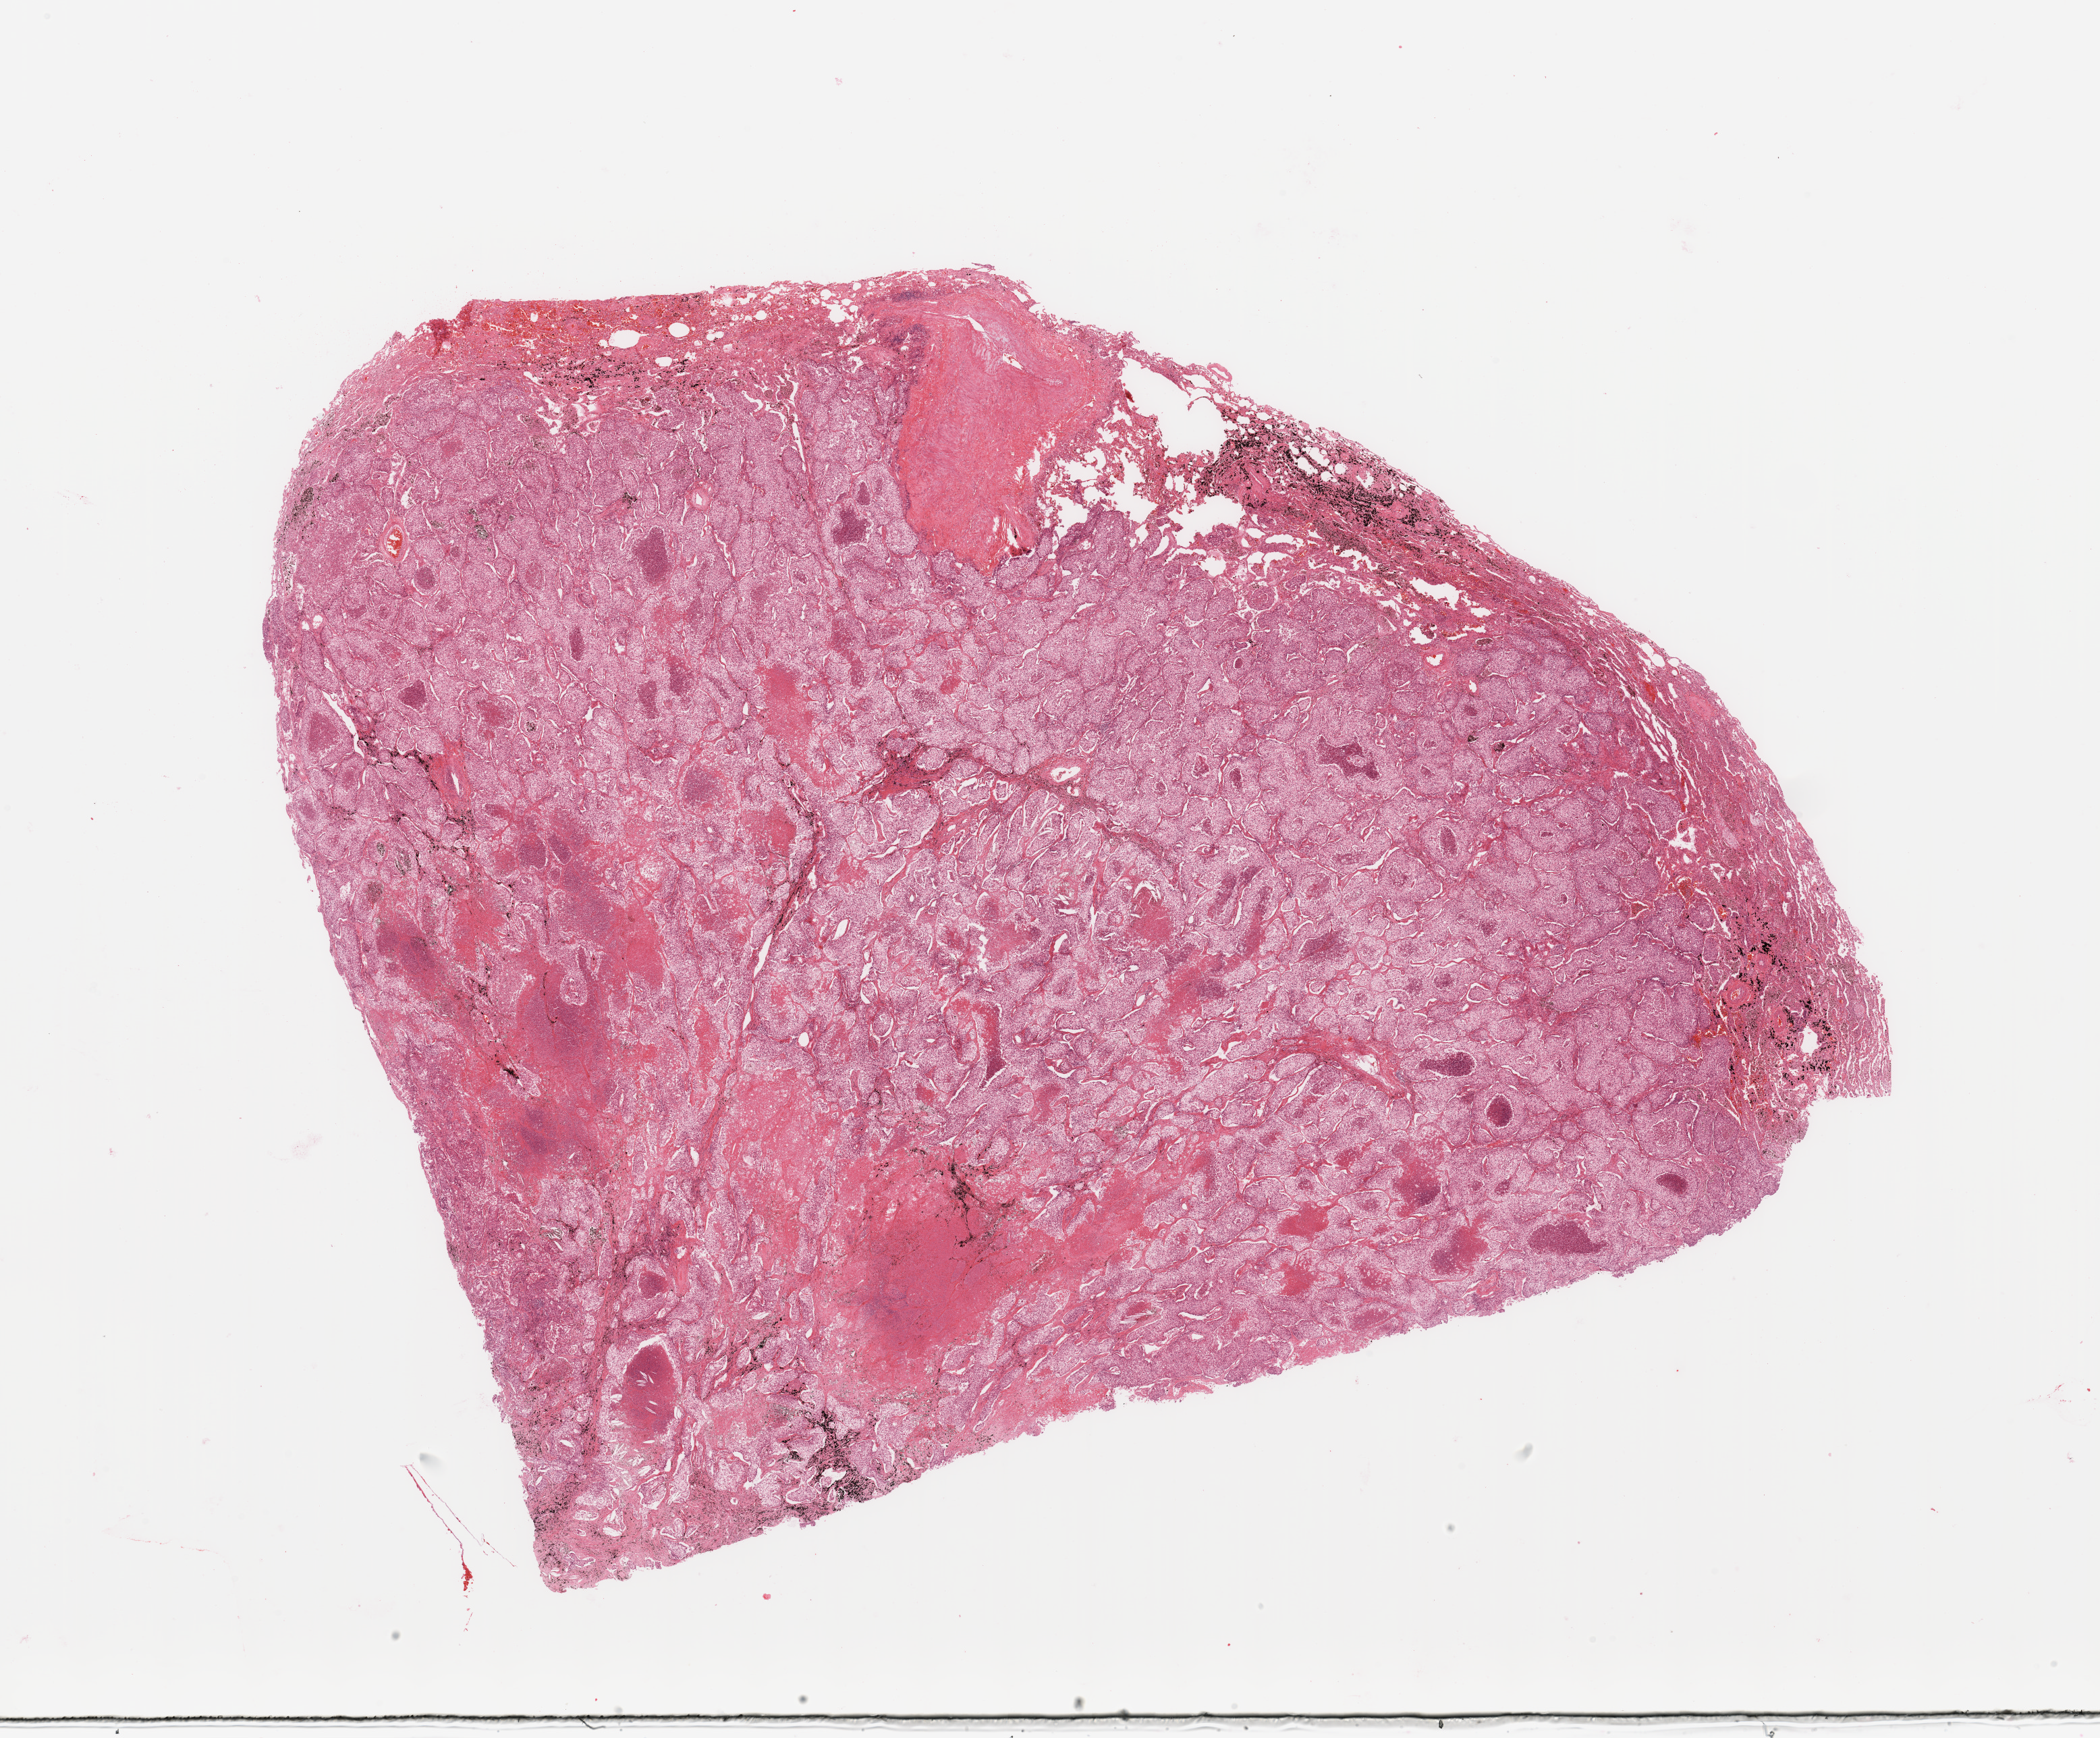
Digitized Hematoxylin and eosin (H&E) stained tissue section (whole slide), low-resolution overview of the scanned area, about 24.6 x 20.4 mm (from a 20x scan); tumour tissue sample, sampled site: lung. Male, 64 y/o. Histologic grade: G3 (poorly differentiated). Composition of this section per pathologist review: tumour nuclei 70%, necrosis 10%.
• diagnosis: Adenocarcinoma, NOS
• AJCC pathologic stage: IIB